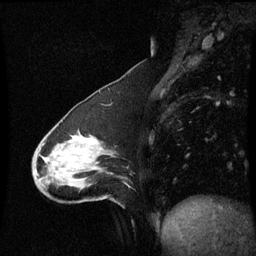
Breast MRI (dynamic contrast-enhanced), one sagittal slice; slice 22 of 60 in the series (ordered by position); dynamic contrast-enhanced series, image 2 of 3 at this slice position (ordered by acquisition); 1.5 T; TE 4.2 ms, TR 8.9 ms; 2 mm slice thickness; 256 × 256 image matrix. Patient: female, 50 years. From the clinical record (not read from this slice): setting: breast cancer imaged before/during neoadjuvant chemotherapy; receptor status: HR-positive, HER2-negative.
Structures marked on this image (semi-automatic segmentation, software-assisted and operator-edited):
- analysis volume of interest (the breast-tissue region the enhancement analysis was run in; not a lesion): bounding box (x1, y1, x2, y2) in pixels: (33, 97, 120, 205)
- tumour enhancement mask (voxels above the 70 % enhancement threshold inside the analysis volume of interest): (92, 139, 96, 141)